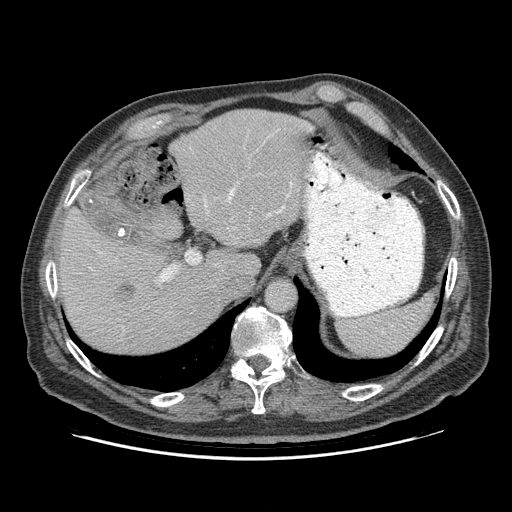
Contrast-enhanced abdominal CT (liver protocol), one axial slice. Slice 68 of 95 in the series (ordered by position). Reconstruction kernel STANDARD. 140 kVp. Soft-tissue window (W 400 / L 40 HU). 512 × 512 image matrix, field of view 400 × 400 mm. From the clinical record (not read from this slice): diagnosis: hepatocellular carcinoma (patient treated with transarterial chemoembolisation; whether this scan precedes or follows treatment is not stated here); TNM stage (as recorded): Stage-IVB; Child-Pugh class: A; tumour differentiation: well differentiated.
Outlined on this slice (semi-automatic segmentation, software-assisted and operator-edited):
- abdominal aorta: bounding box [x1, y1, x2, y2] px = [267, 280, 295, 310]
- liver parenchyma outside the tumour (the mass and vessels are separate outlines, so this box may not span the whole liver): [58, 108, 308, 352]
- mass: [113, 280, 135, 304]
- liver vessels: [90, 183, 292, 282]